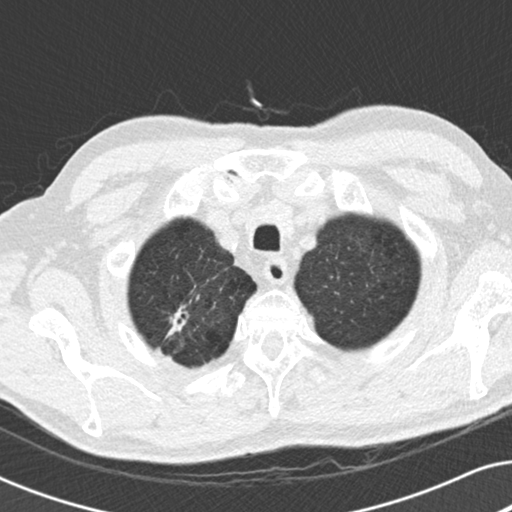
Low-dose screening chest CT, one axial slice. Position 170 of 191 along the scan axis. Reconstruction kernel B30f. 120 kVp. Lung window (W 1500 / L -600 HU). 2 mm slice thickness. 512 × 512 image matrix, field of view 330 × 330 mm.
Outlined on this slice (outlined manually by an expert reader):
- lesion 2 (nodule, lower lobe of right lung): box from (x=167, y=306) to (x=189, y=336) px